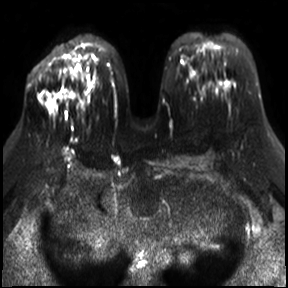
Breast MRI, one axial slice. Position 17 of 30 along the scan axis. Diffusion-weighted series; image 2 of 4 stored at this slice position (different b-values; order by instance number). 3 T. 4 mm slice thickness. 288 × 288 image matrix. Female patient.
Annotated regions visible in this slice (manually delineated by an expert):
- tumour on diffusion-weighted imaging: bounding box <48,100,53,108> (left, top, right, bottom; pixels)